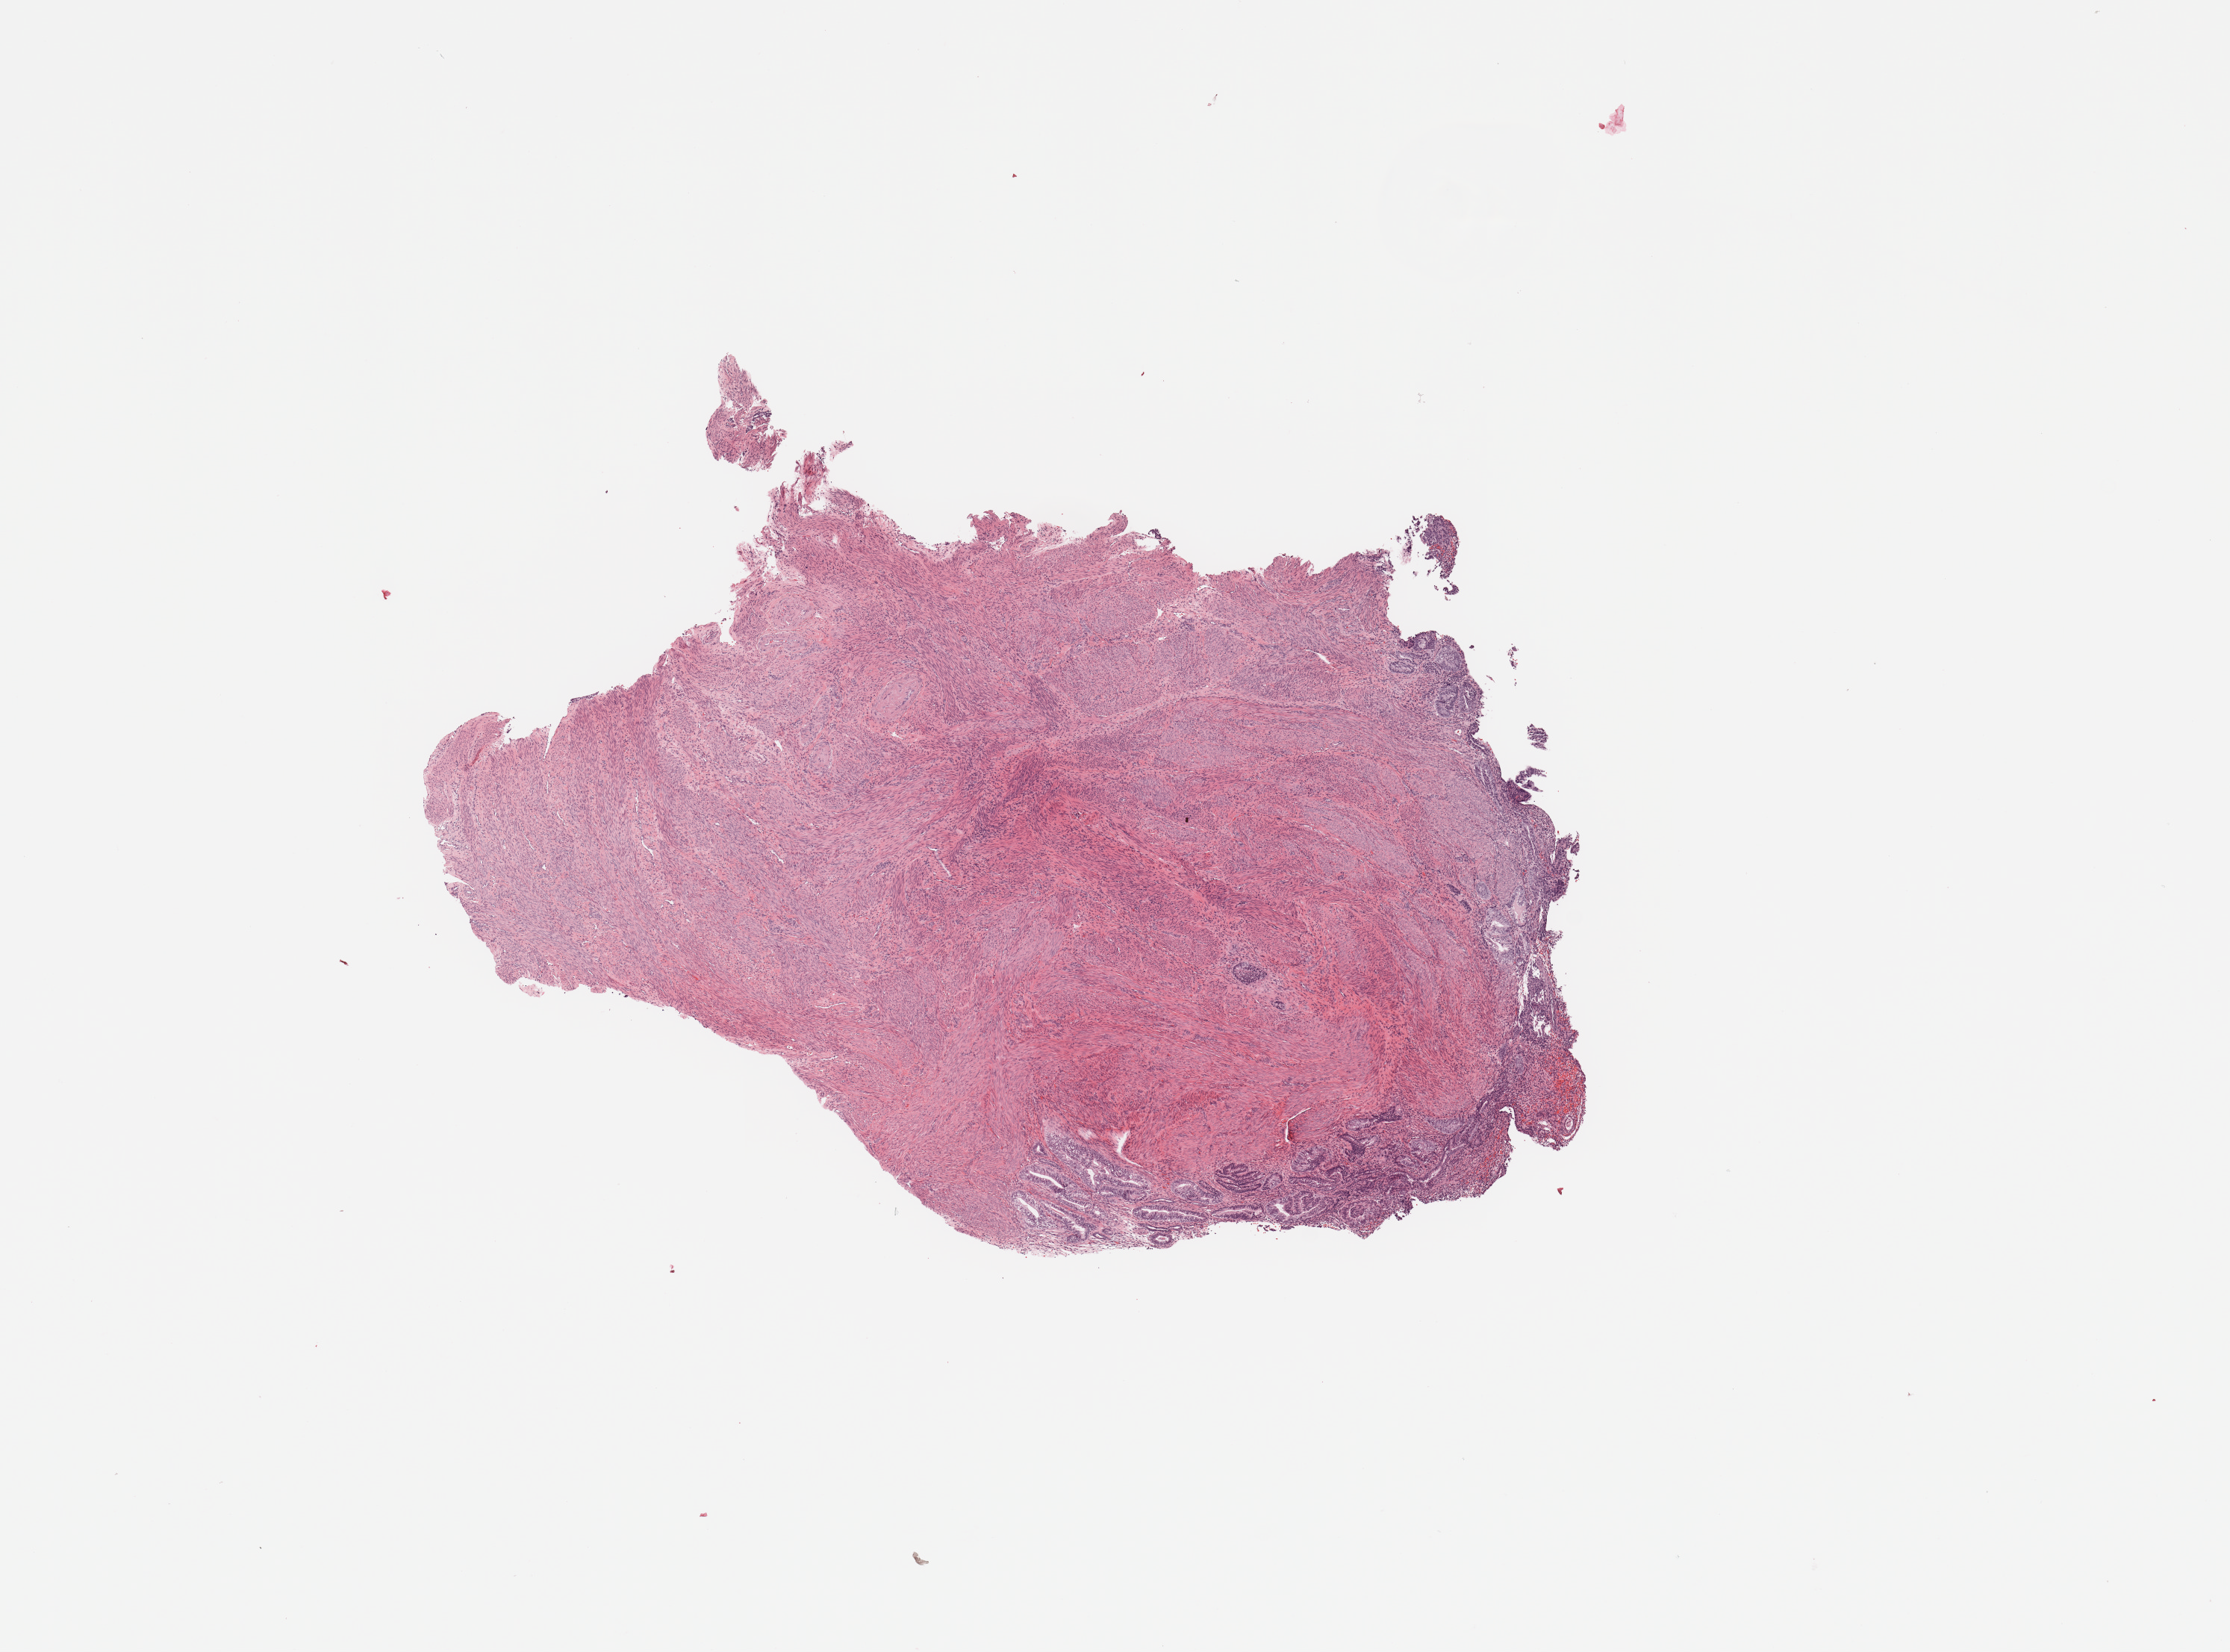
Hematoxylin and eosin (H&E) stained whole-slide image — a low-resolution overview of the entire scanned area, about 11.8 x 8.8 mm (acquisition: 20x scan), normal (non-tumour) tissue sample, sampled site: uterus. Patient: female, age 67 years.
This section: normal (non-tumour) tissue from the same patient. Patient diagnosis: Endometrioid adenocarcinoma, NOS.